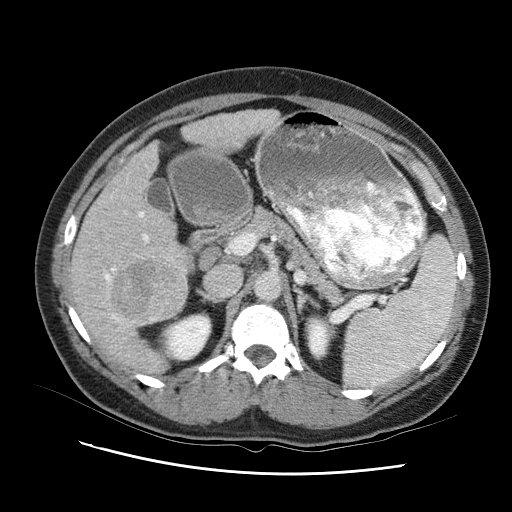
Contrast-enhanced abdominal CT (liver protocol), one axial slice. Slice 51 of 95 in the series (ordered by position). Reconstruction kernel STANDARD. One of 2 acquisitions stored at this slice position. Soft-tissue window (W 400 / L 40 HU). 2.5 mm slice thickness. 512 × 512 image matrix. Case-level facts recorded for this patient, not image findings: diagnosis: hepatocellular carcinoma (patient treated with transarterial chemoembolisation; whether this scan precedes or follows treatment is not stated here); TNM stage (as recorded): Stage-I; Child-Pugh class: B; tumour nodularity: uninodular.
Annotated regions visible in this slice (semi-automatically segmented with operator editing):
- liver parenchyma outside the tumour (the mass and vessels are separate outlines, so this box may not span the whole liver): bounding box (x1, y1, x2, y2) in pixels: (66, 104, 284, 372)
- mass: (115, 255, 191, 320)
- liver vessels: (94, 116, 258, 345)